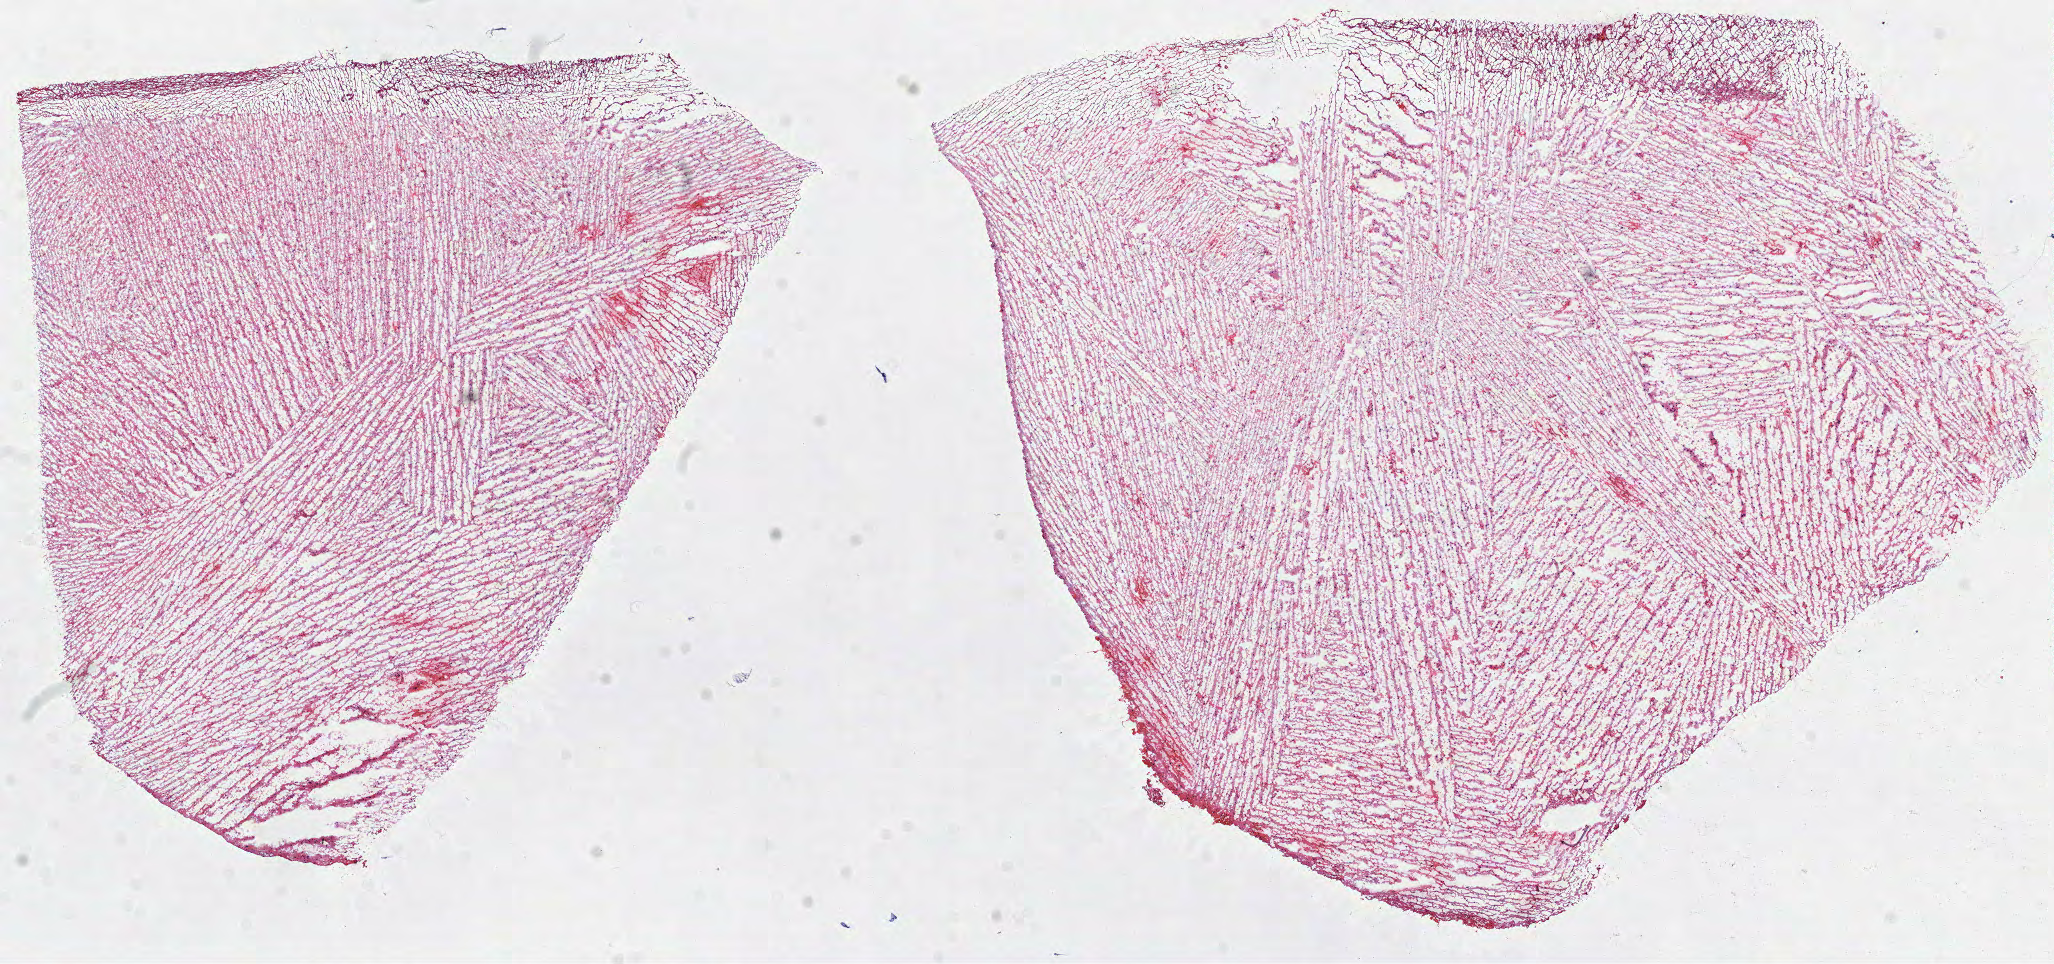
H&E-stained whole-slide image — a low-resolution overview of the entire scanned area, about 16.6 x 7.8 mm; frozen section from the top of the tissue portion; brain, primary tumour sample. Female, age 51 years at initial diagnosis. Histologic grade: G3 (poorly differentiated). Slide review estimates, as recorded: tumour cells 100%, tumour nuclei 65%, normal cells 0%, stromal cells 0%, necrosis 0%.
Pathologic diagnosis: Astrocytoma, anaplastic. Laterality: right.